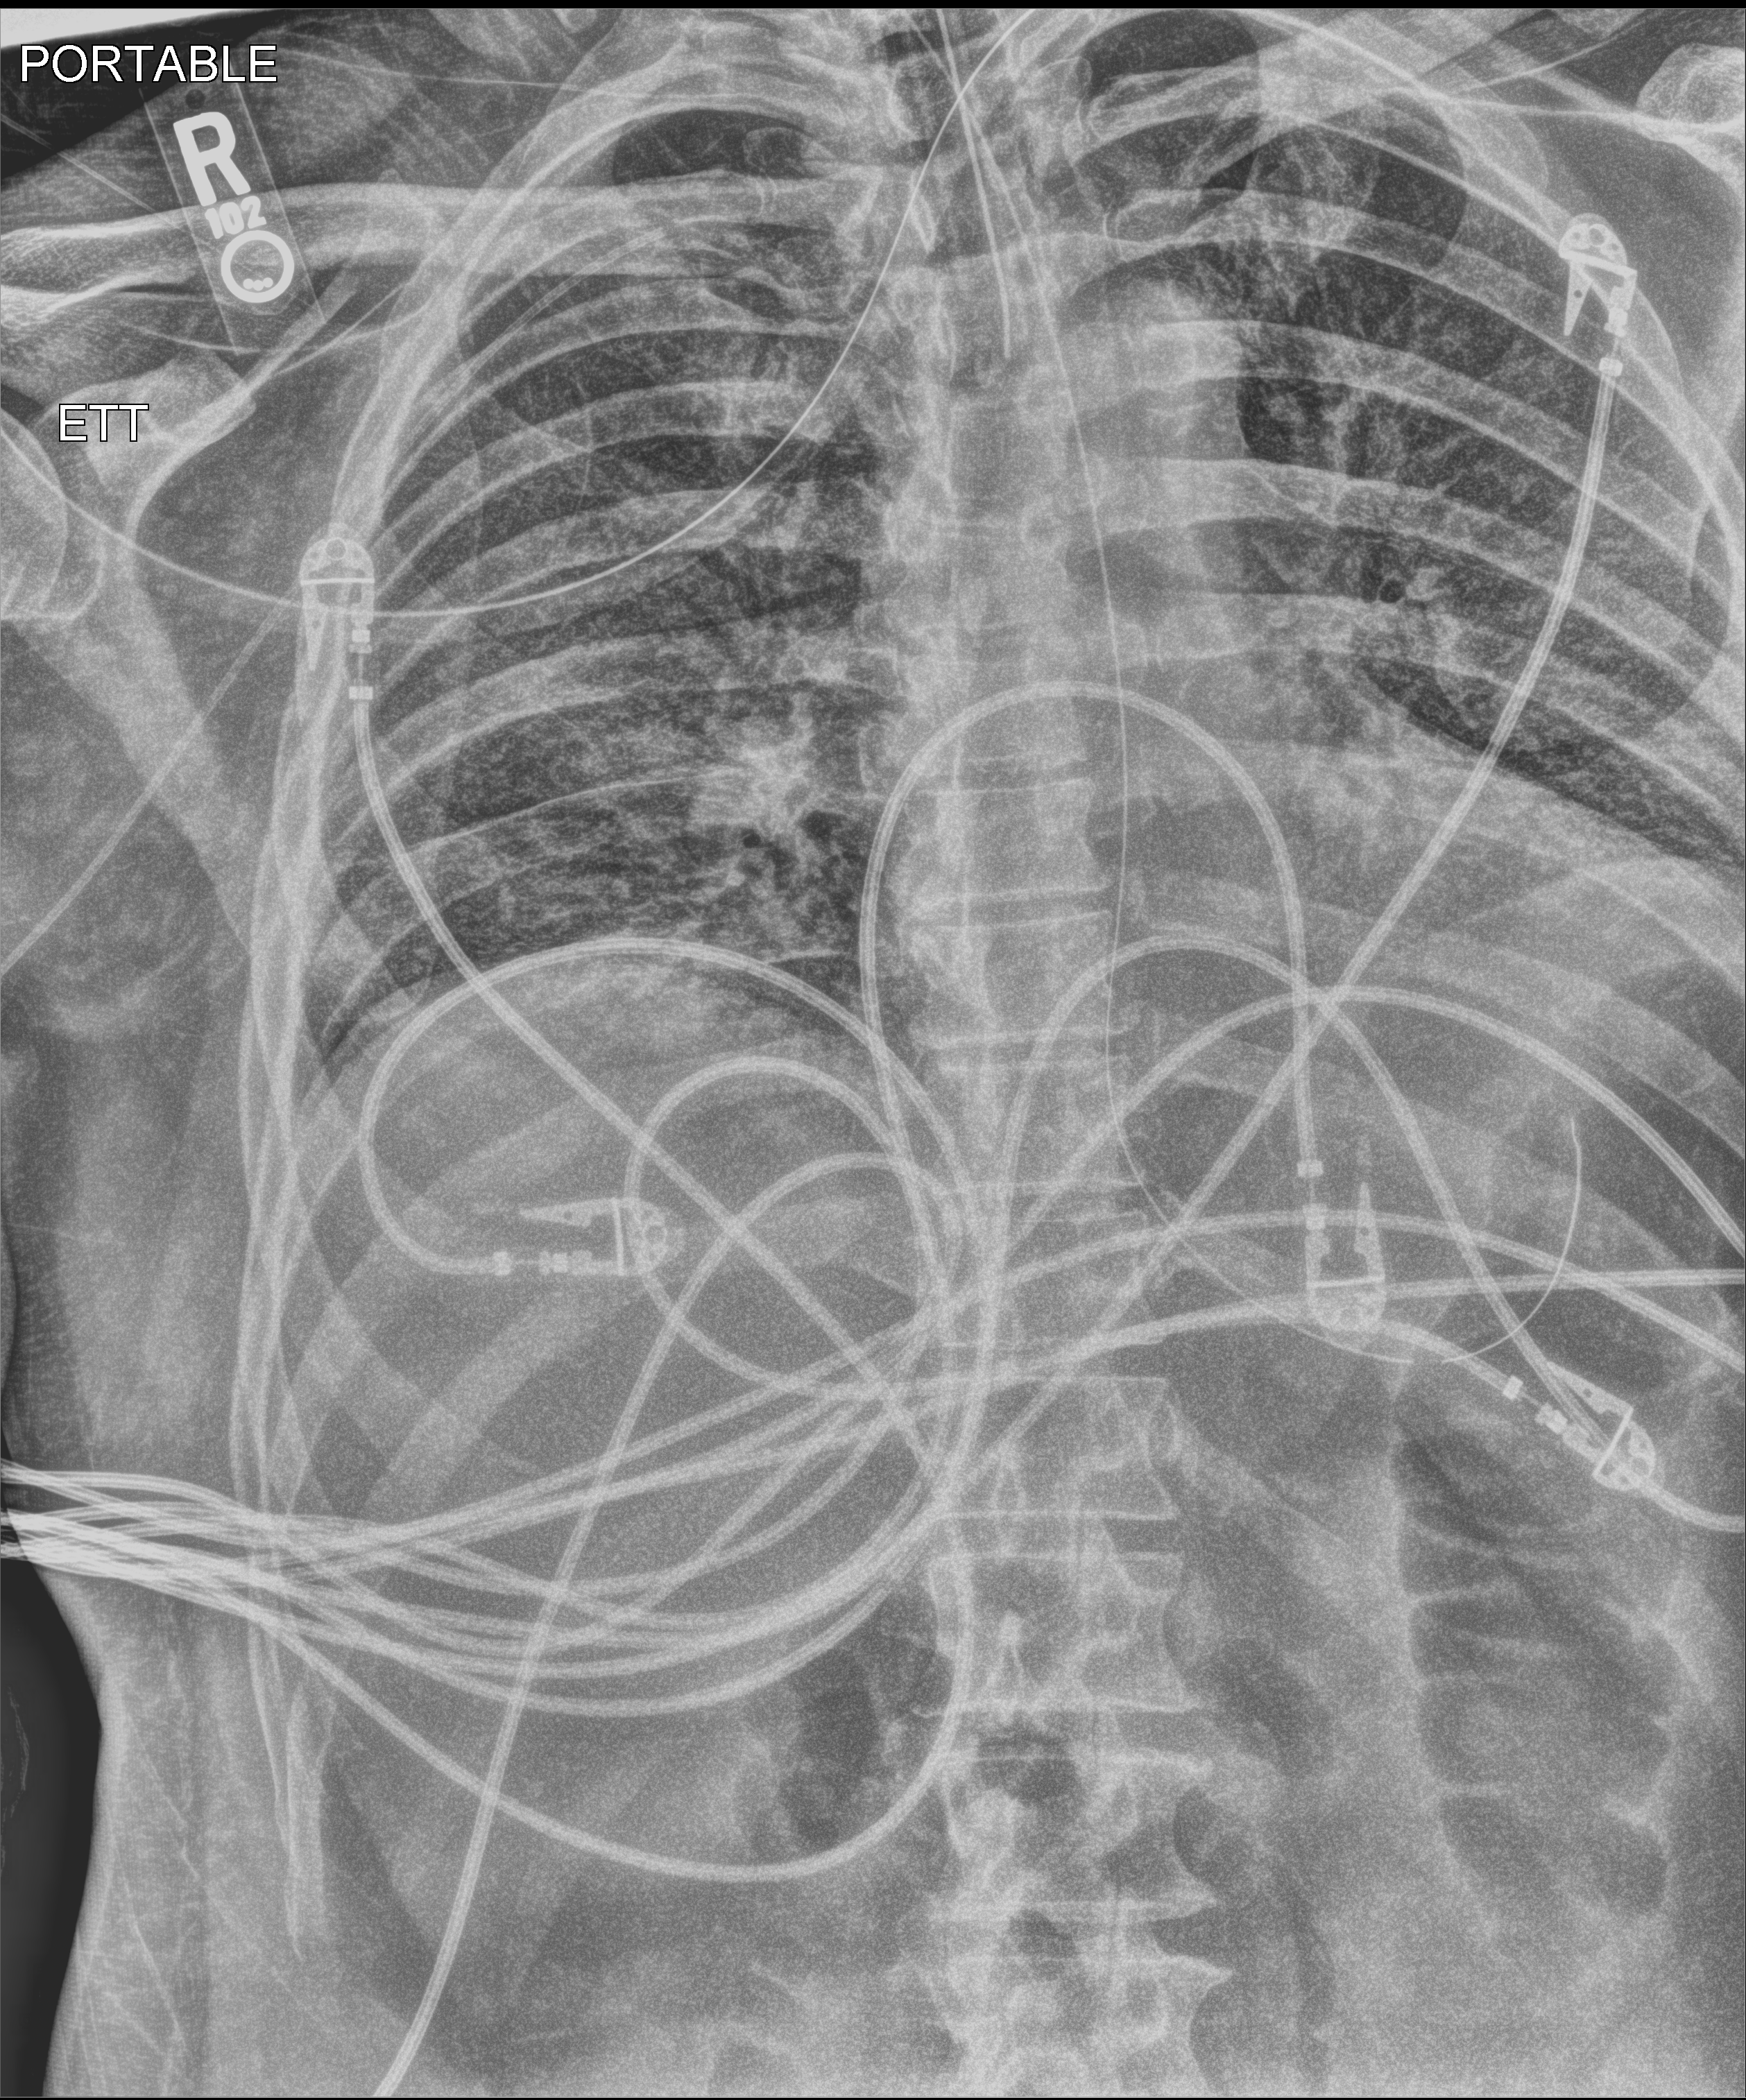
Bedside chest radiograph (computed radiography); anteroposterior (AP) projection. Patient hospitalised with COVID-19; male, aged 60–74 years.
Admission-level facts for this patient (not findings on this image; timing relative to this image not recorded): admitted to intensive care during this hospital stay: yes; chronic kidney disease (admission record): no; smoking status (admission record): never.